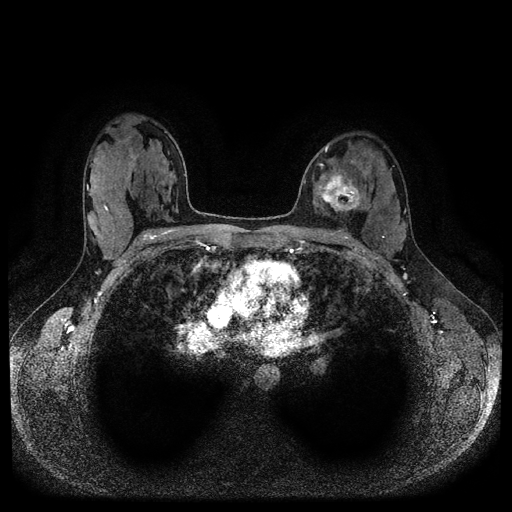
Breast MRI (dynamic contrast-enhanced, multi-phase), one axial slice. Position 62 of 116 along the scan axis. Dynamic contrast-enhanced series, time point 2 of 5 at this slice position (early post-contrast). 1.5 T. TE 2.6 ms, TR 5.3 ms. 2 mm slice thickness. 512 × 512 image matrix. Patient: female, 33 years.
Outlined on this slice (semi-automatically segmented with operator editing):
- breast lesion (labelled 'tumour' in the annotation; benign lesions carry a separate 'benign' label): bounding box (x1, y1, x2, y2) in pixels: (317, 169, 363, 215)